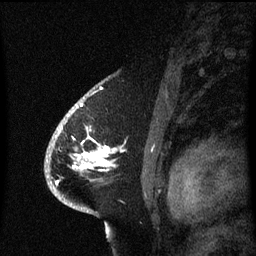
Breast MRI (dynamic contrast-enhanced), one sagittal slice; position 45 of 60 along the scan axis; dynamic contrast-enhanced series, image 2 of 3 at this slice position (ordered by acquisition); 1.5 T; TE 4.2 ms, TR 8.4 ms; 2.1 mm slice thickness; 256 × 256 image matrix, field of view 200 × 200 mm. Patient: female, 53 years. From the clinical record (not read from this slice): setting: breast cancer imaged before/during neoadjuvant chemotherapy; receptor status: HR-positive, HER2-negative.
Structures marked on this image (semi-automatically segmented with operator editing):
- analysis volume of interest (the breast-tissue region the enhancement analysis was run in; not a lesion): box from (x=49, y=108) to (x=124, y=201) px
- tumour enhancement mask (voxels above the 70 % enhancement threshold inside the analysis volume of interest): (x=76, y=148)–(x=112, y=169)